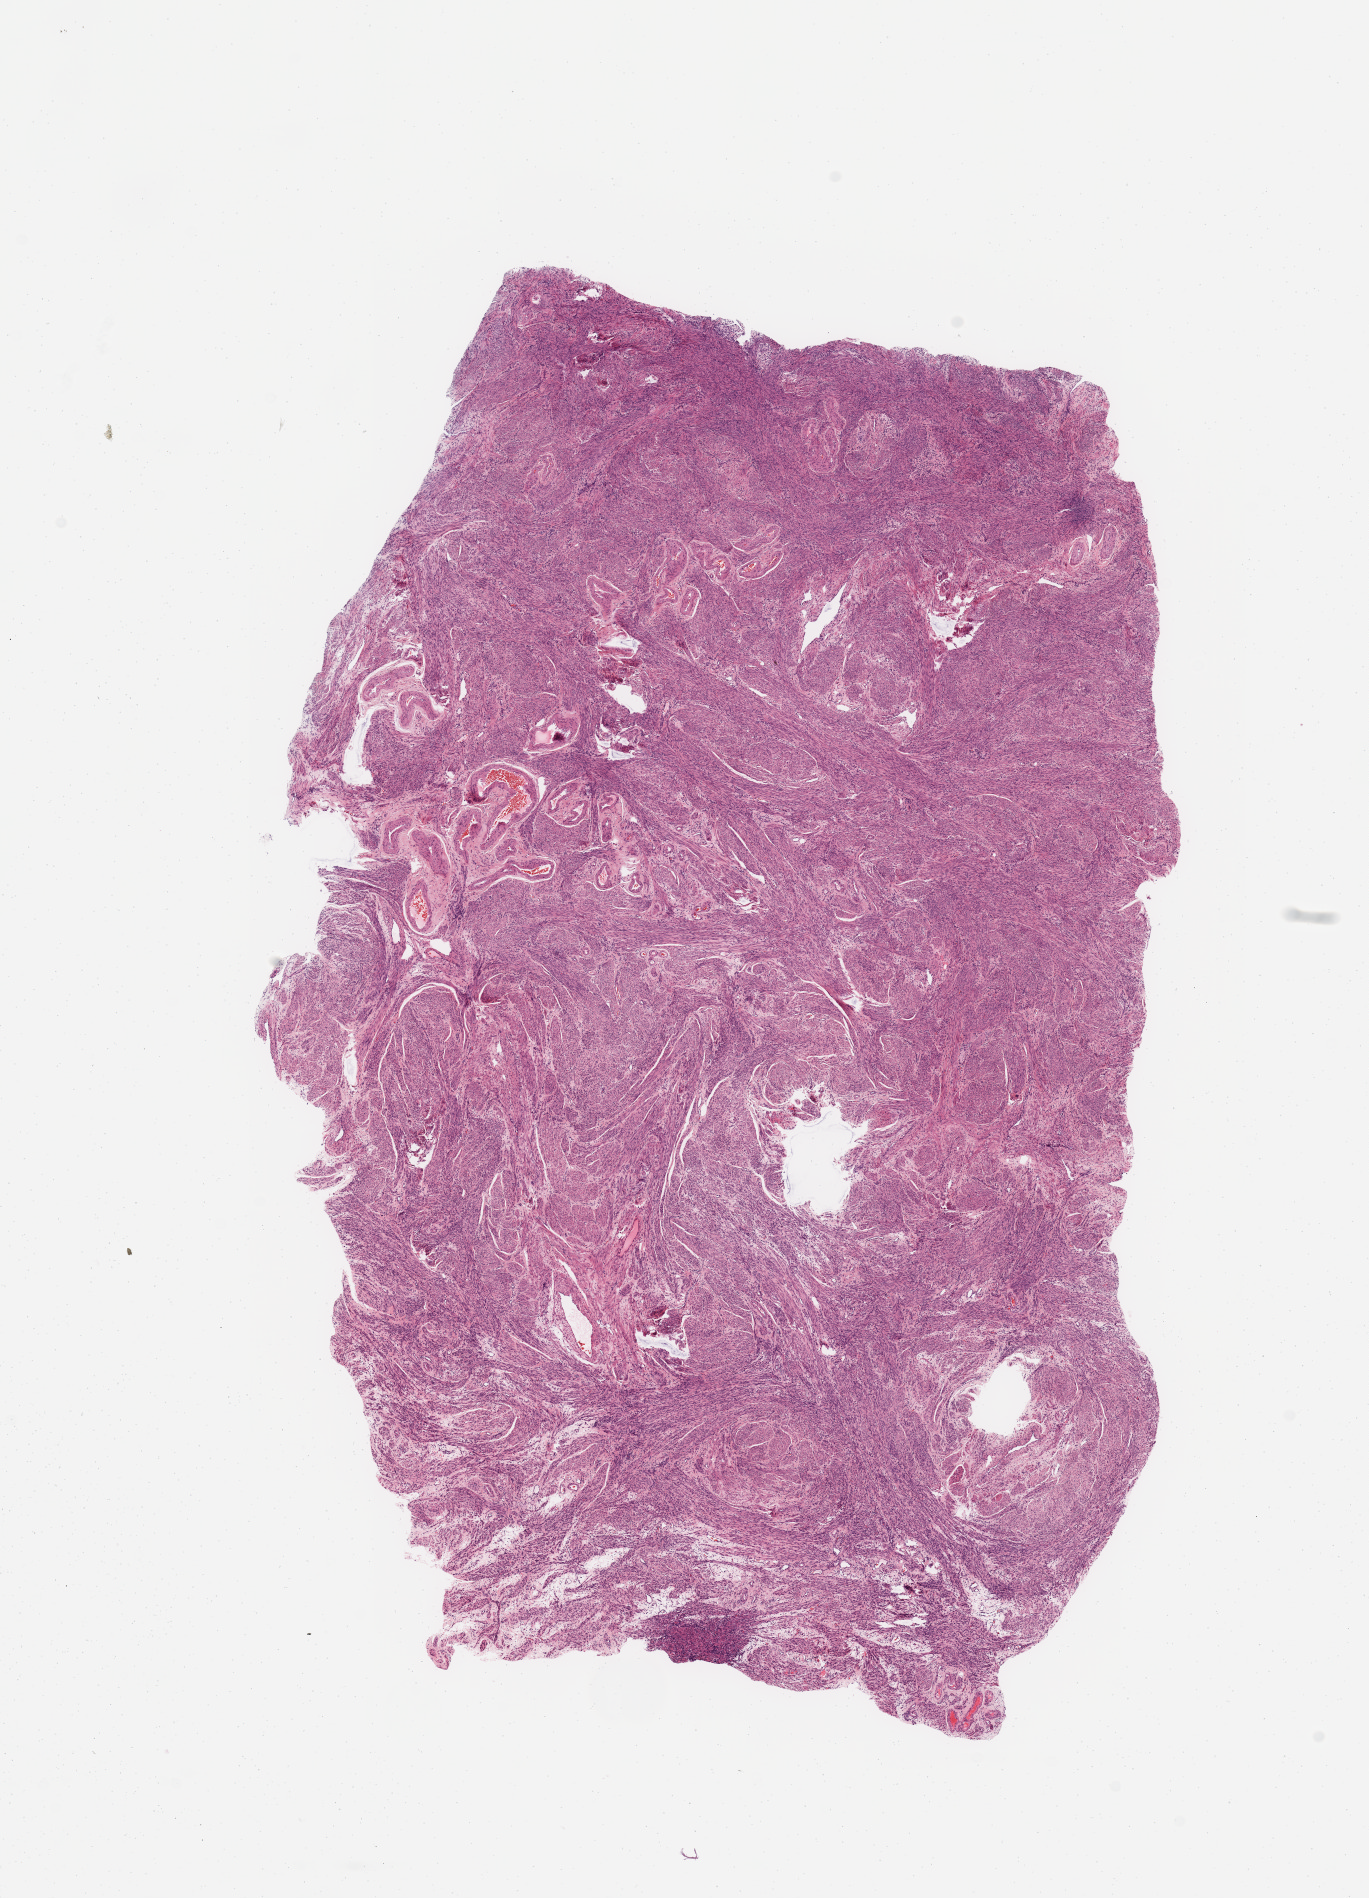
Digitized H&E tissue section (whole slide), a low-resolution overview of the entire scanned area, about 10.8 x 15.0 mm (slide scanned at 20x); normal (non-tumour) tissue sample, uterus. 60-year-old female patient.
* this section: normal (non-tumour) tissue from the same patient
* patient diagnosis: Endometrioid adenocarcinoma, NOS